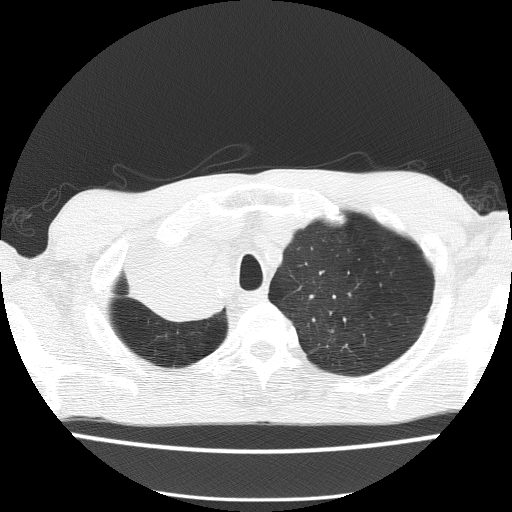
Low-dose screening chest CT, one axial slice. Slice 125 of 150 in the series (ordered by position). Lung window (W 1500 / L -600 HU). 2 mm slice thickness. 512 × 512 image matrix.
Structures marked on this image (expert manual segmentation):
- lesion 1 (tumor, hilum of right lung): bounding box <129,238,223,320> (left, top, right, bottom; pixels)